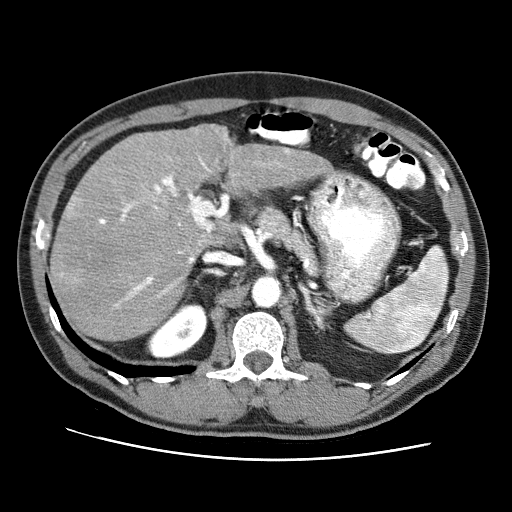
Contrast-enhanced abdominal CT (liver protocol), one axial slice. Position 46 of 71 along the scan axis. Soft-tissue window (W 400 / L 40 HU). 2.5 mm slice thickness. 512 × 512 image matrix, field of view 360 × 360 mm. Case-level facts recorded for this patient, not image findings: diagnosis: hepatocellular carcinoma (patient treated with transarterial chemoembolisation; whether this scan precedes or follows treatment is not stated here); TNM stage (as recorded): Stage-II; Child-Pugh class: A; tumour nodularity: multinodular; tumour size: 4.6 cm.
Annotated regions visible in this slice (semi-automatic segmentation, software-assisted and operator-edited):
- liver parenchyma outside the tumour (the mass and vessels are separate outlines, so this box may not span the whole liver): bounding box [x1, y1, x2, y2] px = [50, 124, 328, 342]
- liver vessels: [99, 150, 288, 300]